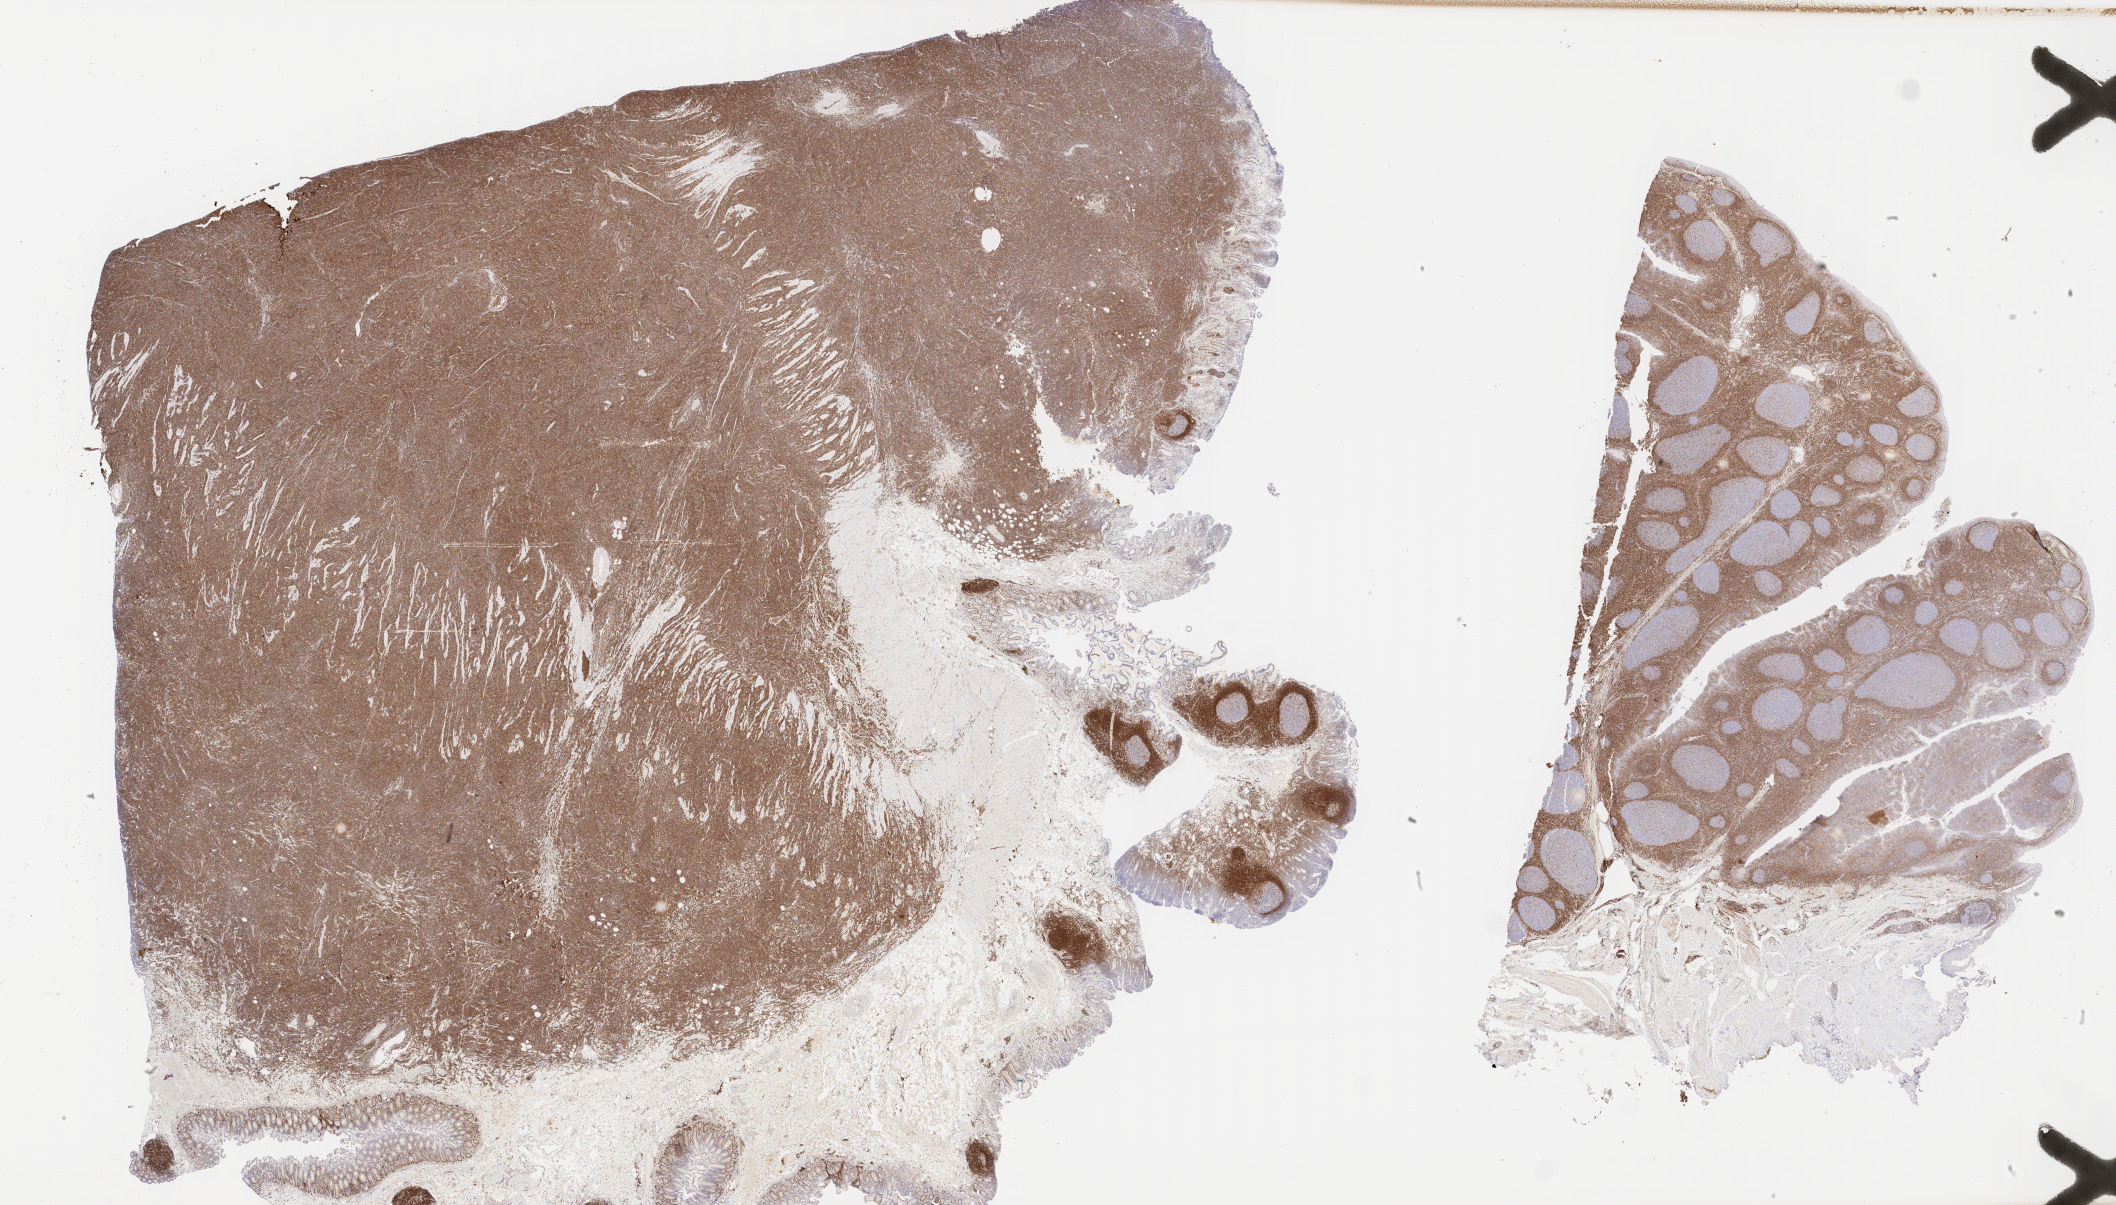
IHC for BCL2, whole-slide image, shown as a low-resolution overview of the whole scanned area (about 34.2 x 19.5 mm); tumor tissue. Patient male; age 59 years.
Histologic diagnosis: Burkitt lymphoma, NOS.